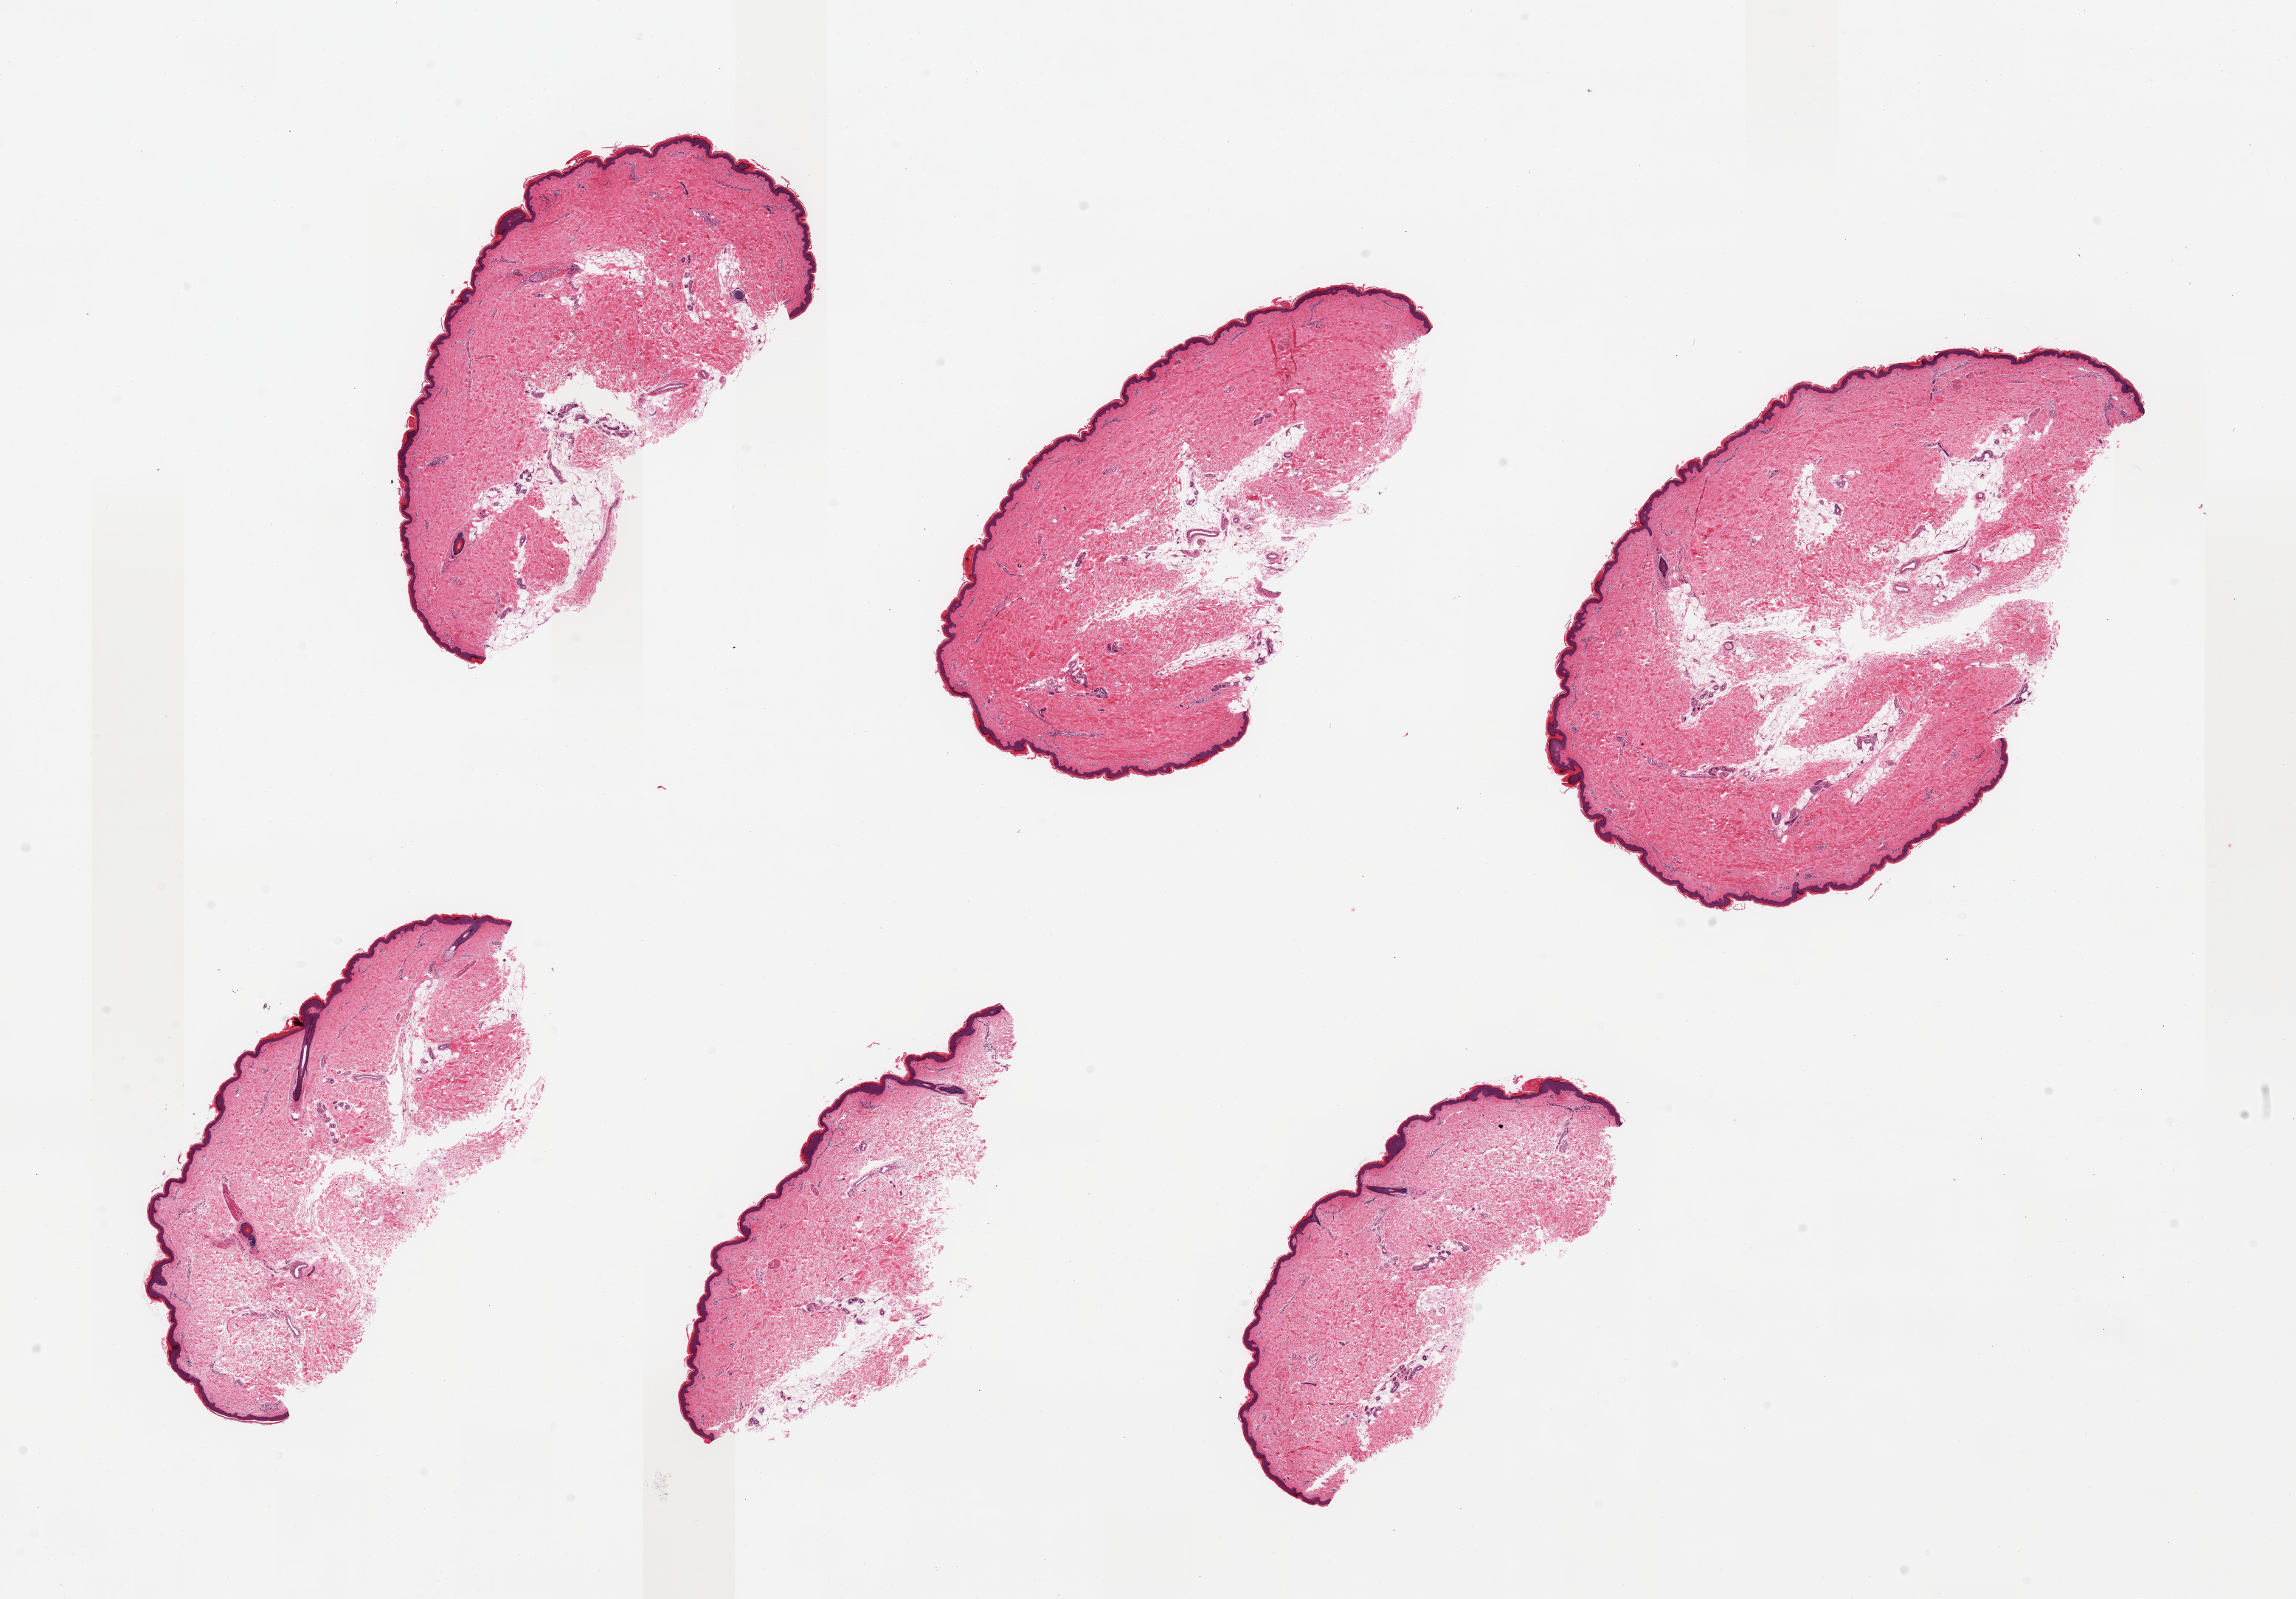
Whole-slide image, H&E stain — a low-resolution overview of the entire scanned area, about 24.6 x 17.1 mm; PAXgene-fixed, paraffin-embedded tissue; sampled site (target tissue): skin of lower leg; tissue donor sample. Donor sex: female.
Pathologist's review note for this sample: 6 pieces; 10-20% dermal fat.